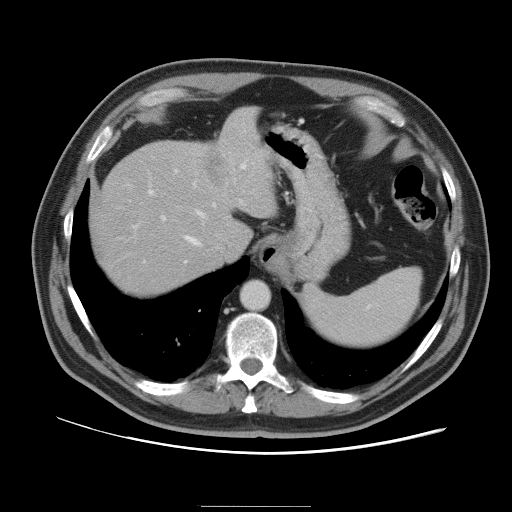
Contrast-enhanced abdominal CT, one axial slice; position 79 of 105 along the scan axis; 120 kVp; intravenous contrast given; soft-tissue window (W 400 / L 40 HU); 5 mm slice thickness; 512 × 512 image matrix, field of view 399 × 399 mm. Male patient, age 64 years. Case-level facts recorded for this patient, not image findings: diagnosis: colorectal cancer liver metastases, imaged before liver resection; multiple liver metastases: yes; largest metastasis: 3 cm; disease in both lobes: yes.
Structures marked on this image (manually delineated by an expert):
- hepatic veins: bounding box <184,209,206,246> (left, top, right, bottom; pixels)
- liver: <92,109,272,295>
- planned liver remnant (the part of the liver to remain after resection): <92,148,229,294>
- portal vein (with intrahepatic branches): <133,164,246,263>
- liver metastasis: <208,151,221,181>